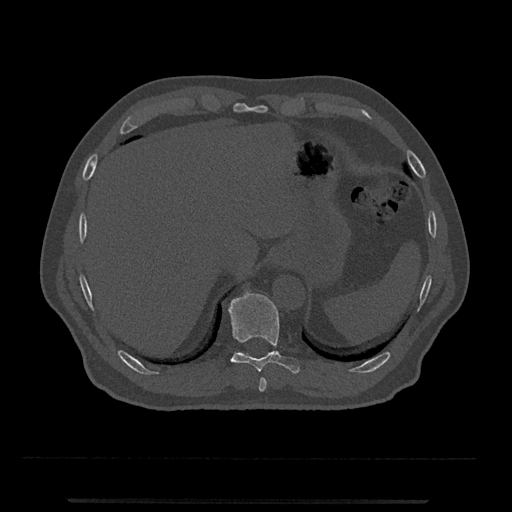
CT including the spine, one axial slice. Position 515 of 797 along the scan axis. Reconstruction kernel Br40s/3. 120 kVp. Bone window (W 1800 / L 400 HU). 0.5 mm slice thickness. 512 × 512 image matrix, field of view 419 × 419 mm. Male patient, age 63 years. From the clinical record (not read from this slice): primary cancer: prostate.
Annotated regions visible in this slice (semi-automatic segmentation, software-assisted and operator-edited):
- T10 vertebra: bounding box <228,291,300,374> (left, top, right, bottom; pixels)
- T9 vertebra: <259,377,267,392>